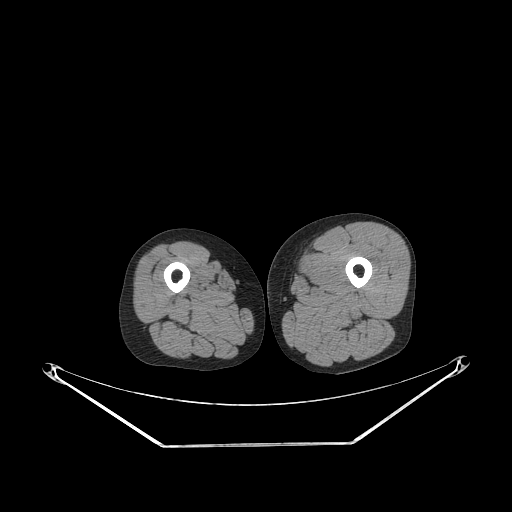
CT of an extremity soft-tissue mass (from a PET/CT study), one axial slice. Reconstruction kernel STANDARD. 140 kVp. Soft-tissue window (W 400 / L 40 HU). 3.75 mm slice thickness. 512 × 512 image matrix, field of view 500 × 500 mm. Male patient. From the clinical record (not read from this slice): histological type: pleiomorphic leiomyosarcoma; grade: high; site of the primary tumour: left thigh.
Annotated regions visible in this slice (expert contour drawn on MRI and transferred to this co-registered scan by the dataset authors):
- gross tumour volume including surrounding oedema: bounding box <292,262,309,284> (left, top, right, bottom; pixels)